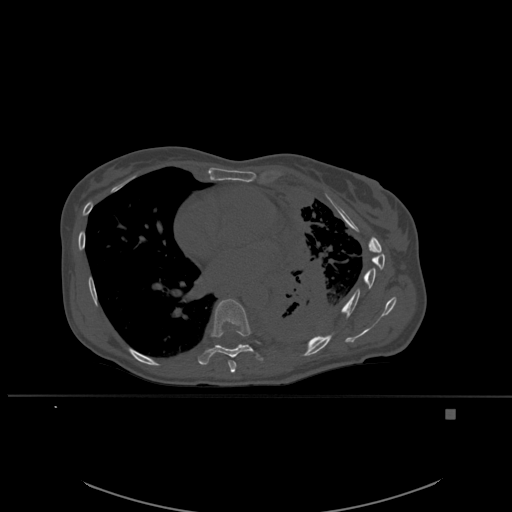
CT including the spine, one axial slice; position 350 of 537 along the scan axis; bone window (W 1800 / L 400 HU); 1.5 mm slice thickness; 512 × 512 image matrix, field of view 440 × 440 mm. Female patient, age 45 years. From the clinical record (not read from this slice): primary cancer: lung.
Annotated regions visible in this slice (semi-automatically segmented with operator editing):
- T7 vertebra: bounding box [x1, y1, x2, y2] px = [228, 360, 237, 373]
- T8 vertebra: [198, 298, 264, 365]